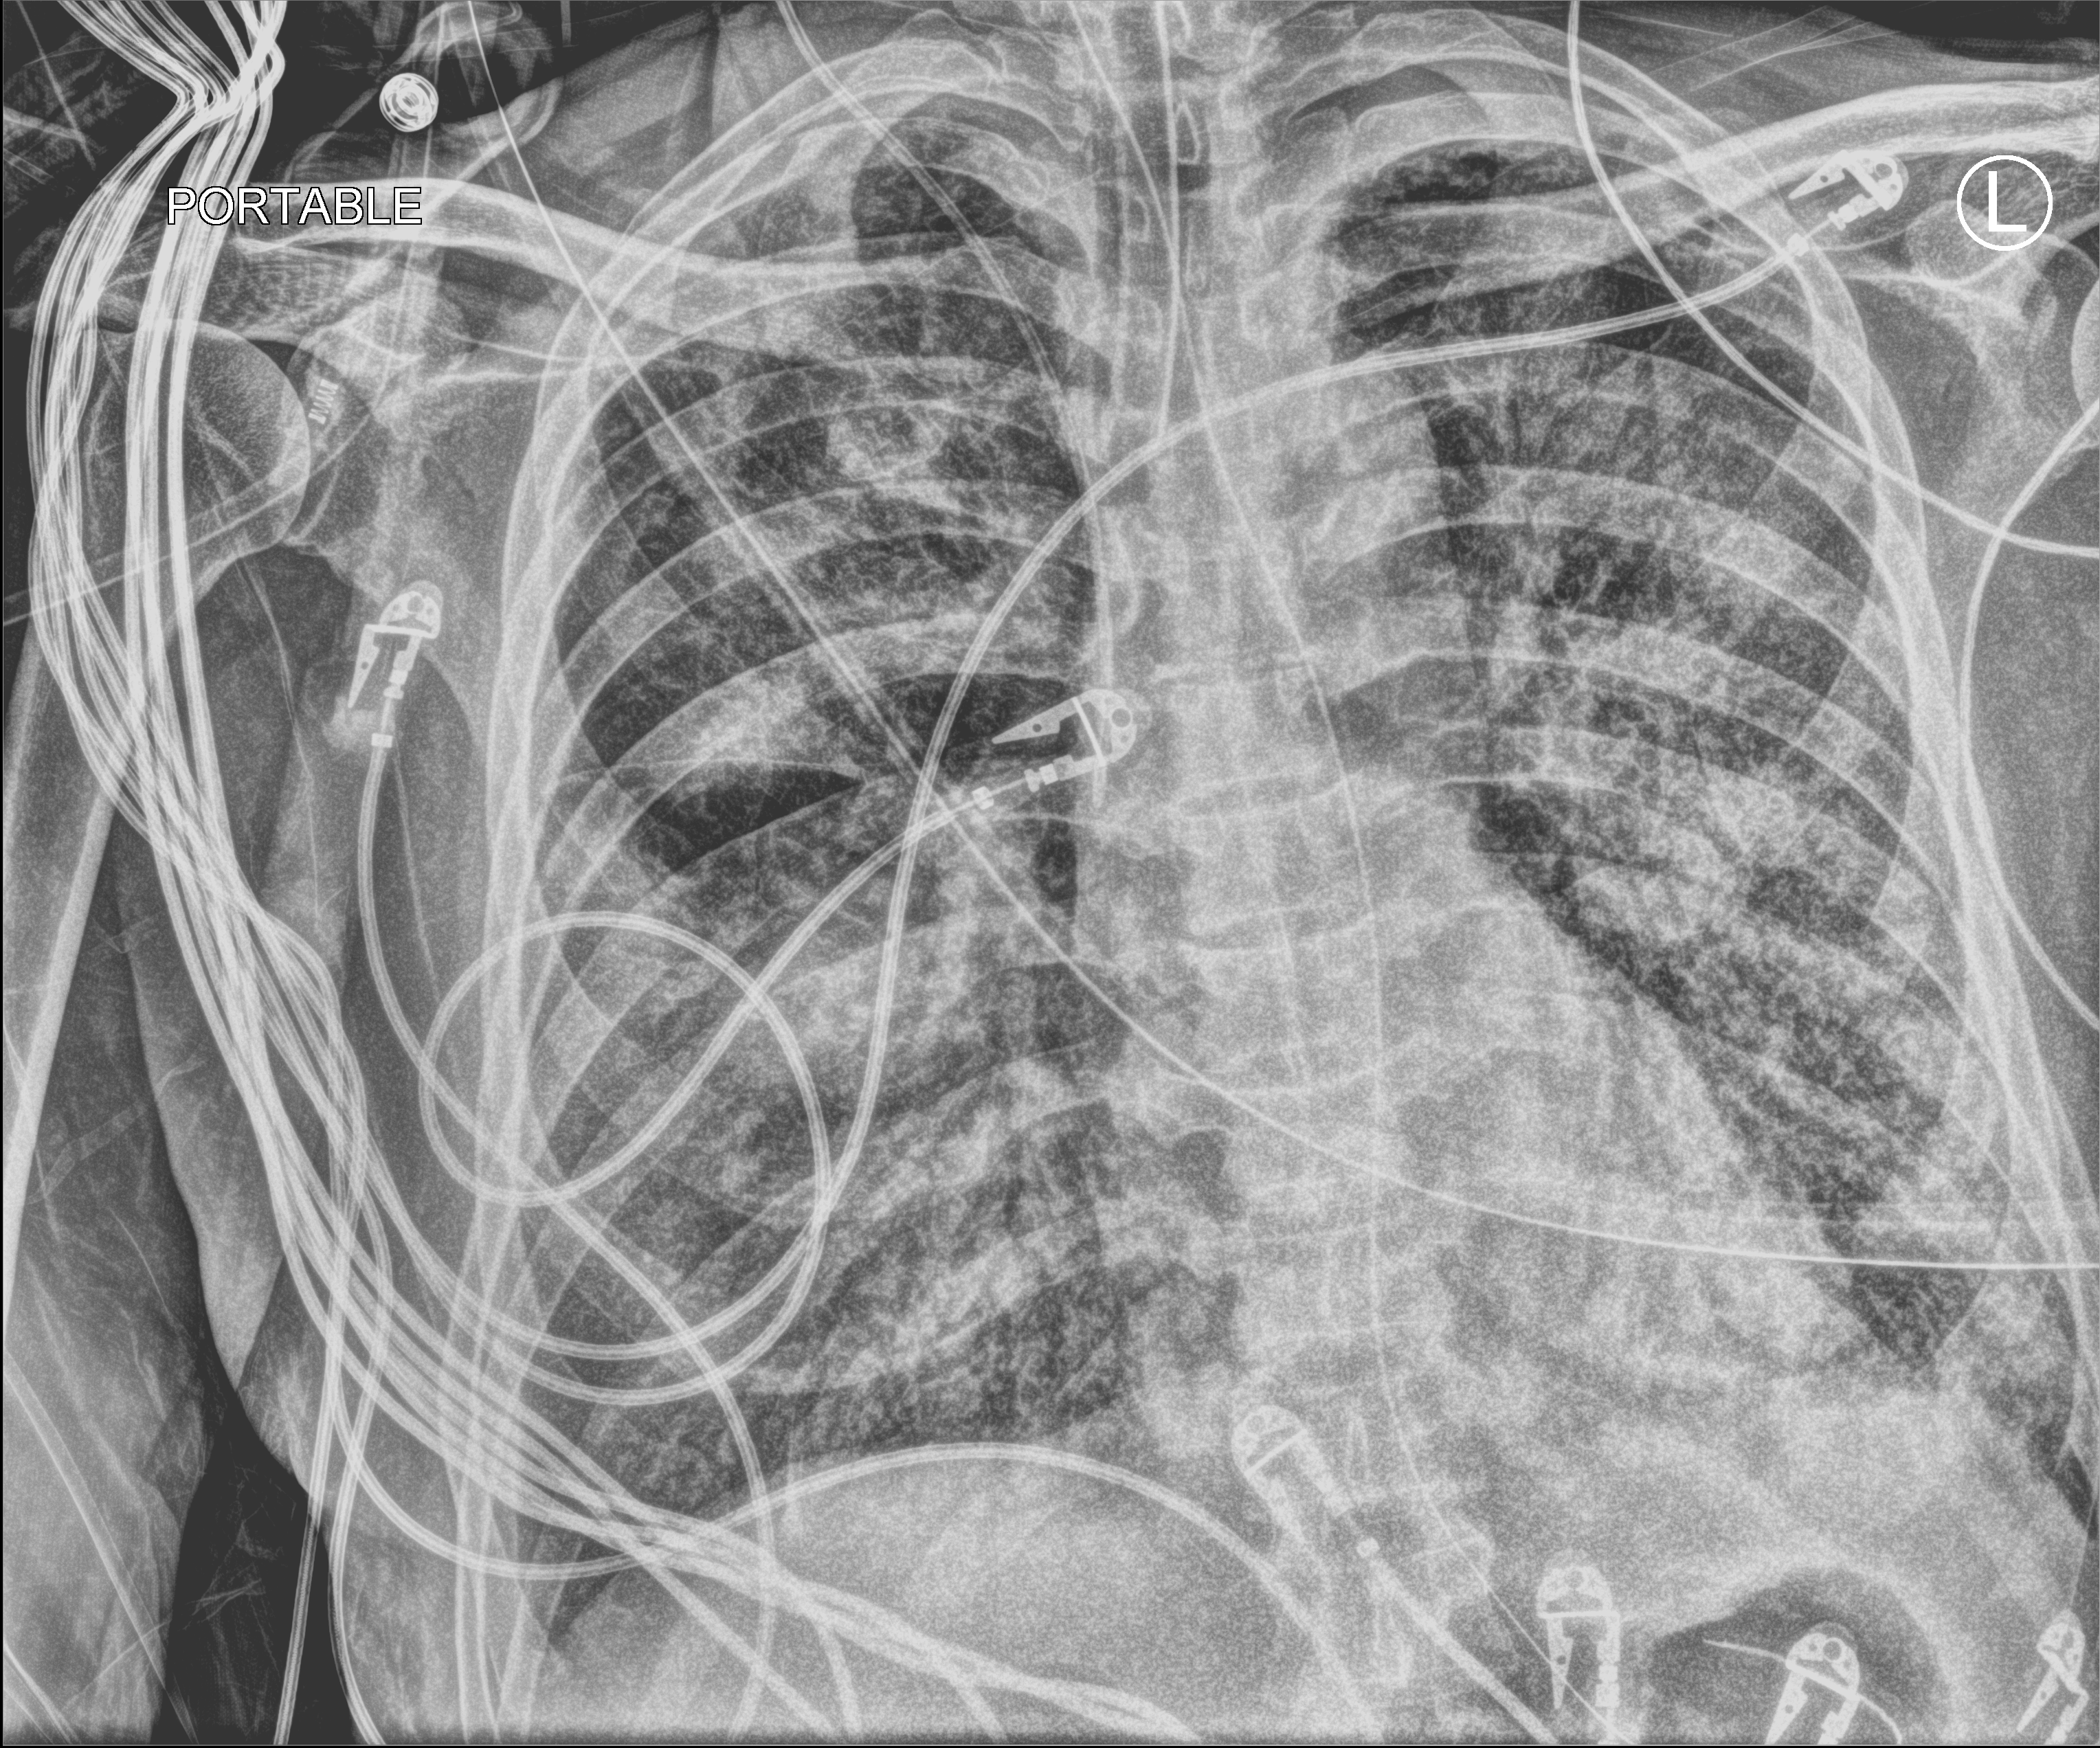
Bedside chest radiograph (computed radiography), anteroposterior (AP) projection. Male patient hospitalised with COVID-19, age 60–74 years.
Admission-level facts for this patient (not findings on this image; timing relative to this image not recorded):
- admitted to intensive care during this hospital stay: yes